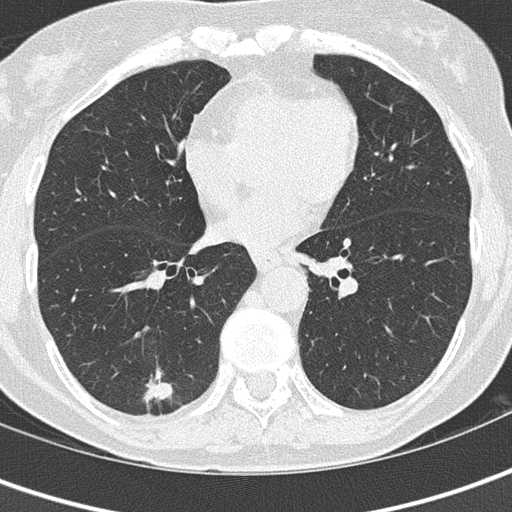
Chest CT (low-dose screening protocol), one axial image; second annual screen; lung window (W 1500 / L -600 HU). Female, age 69 years at enrolment. Current smoker at enrolment.
Lesion marked by an expert reader, box from (x=121, y=363) to (x=182, y=423) px. The screening reader recorded 2 non-calcified nodules or masses ≥4 mm on this exam (right lower lobe, left lower lobe); which of them this box marks is not recorded. Later outcome: lung cancer diagnosed 112 days after this screen — adenocarcinoma, NOS, right lower lobe, moderately differentiated (G2), stage IA (AJCC 6th edition), 16 mm at pathology.